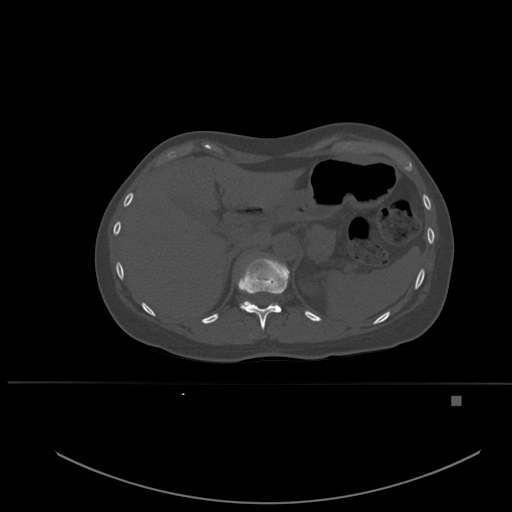
CT including the spine, one axial slice; position 268 of 651 along the scan axis; bone window (W 1800 / L 400 HU); 1.5 mm slice thickness; 512 × 512 image matrix, field of view 443 × 443 mm. Patient: female, 49 years. From the clinical record (not read from this slice): primary cancer: breast.
Structures marked on this image (semi-automatically segmented with operator editing):
- T11 vertebra: bounding box <238,257,290,330> (left, top, right, bottom; pixels)
- T12 vertebra: <240,293,274,308>